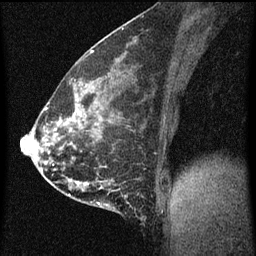
Breast MRI (dynamic contrast-enhanced), one sagittal slice. Position 25 of 60 along the scan axis. Dynamic contrast-enhanced series, image 2 of 3 at this slice position (ordered by acquisition). 1.5 T. TE 4.2 ms, TR 8 ms. 2 mm slice thickness. 256 × 256 image matrix, field of view 180 × 180 mm. Patient: female, 35 years.
Outlined on this slice (semi-automatic segmentation, software-assisted and operator-edited):
- analysis volume of interest (the breast-tissue region the enhancement analysis was run in; not a lesion): bounding box <110,180,145,217> (left, top, right, bottom; pixels)
- tumour enhancement mask (voxels above the 70 % enhancement threshold inside the analysis volume of interest): <110,184,120,191>